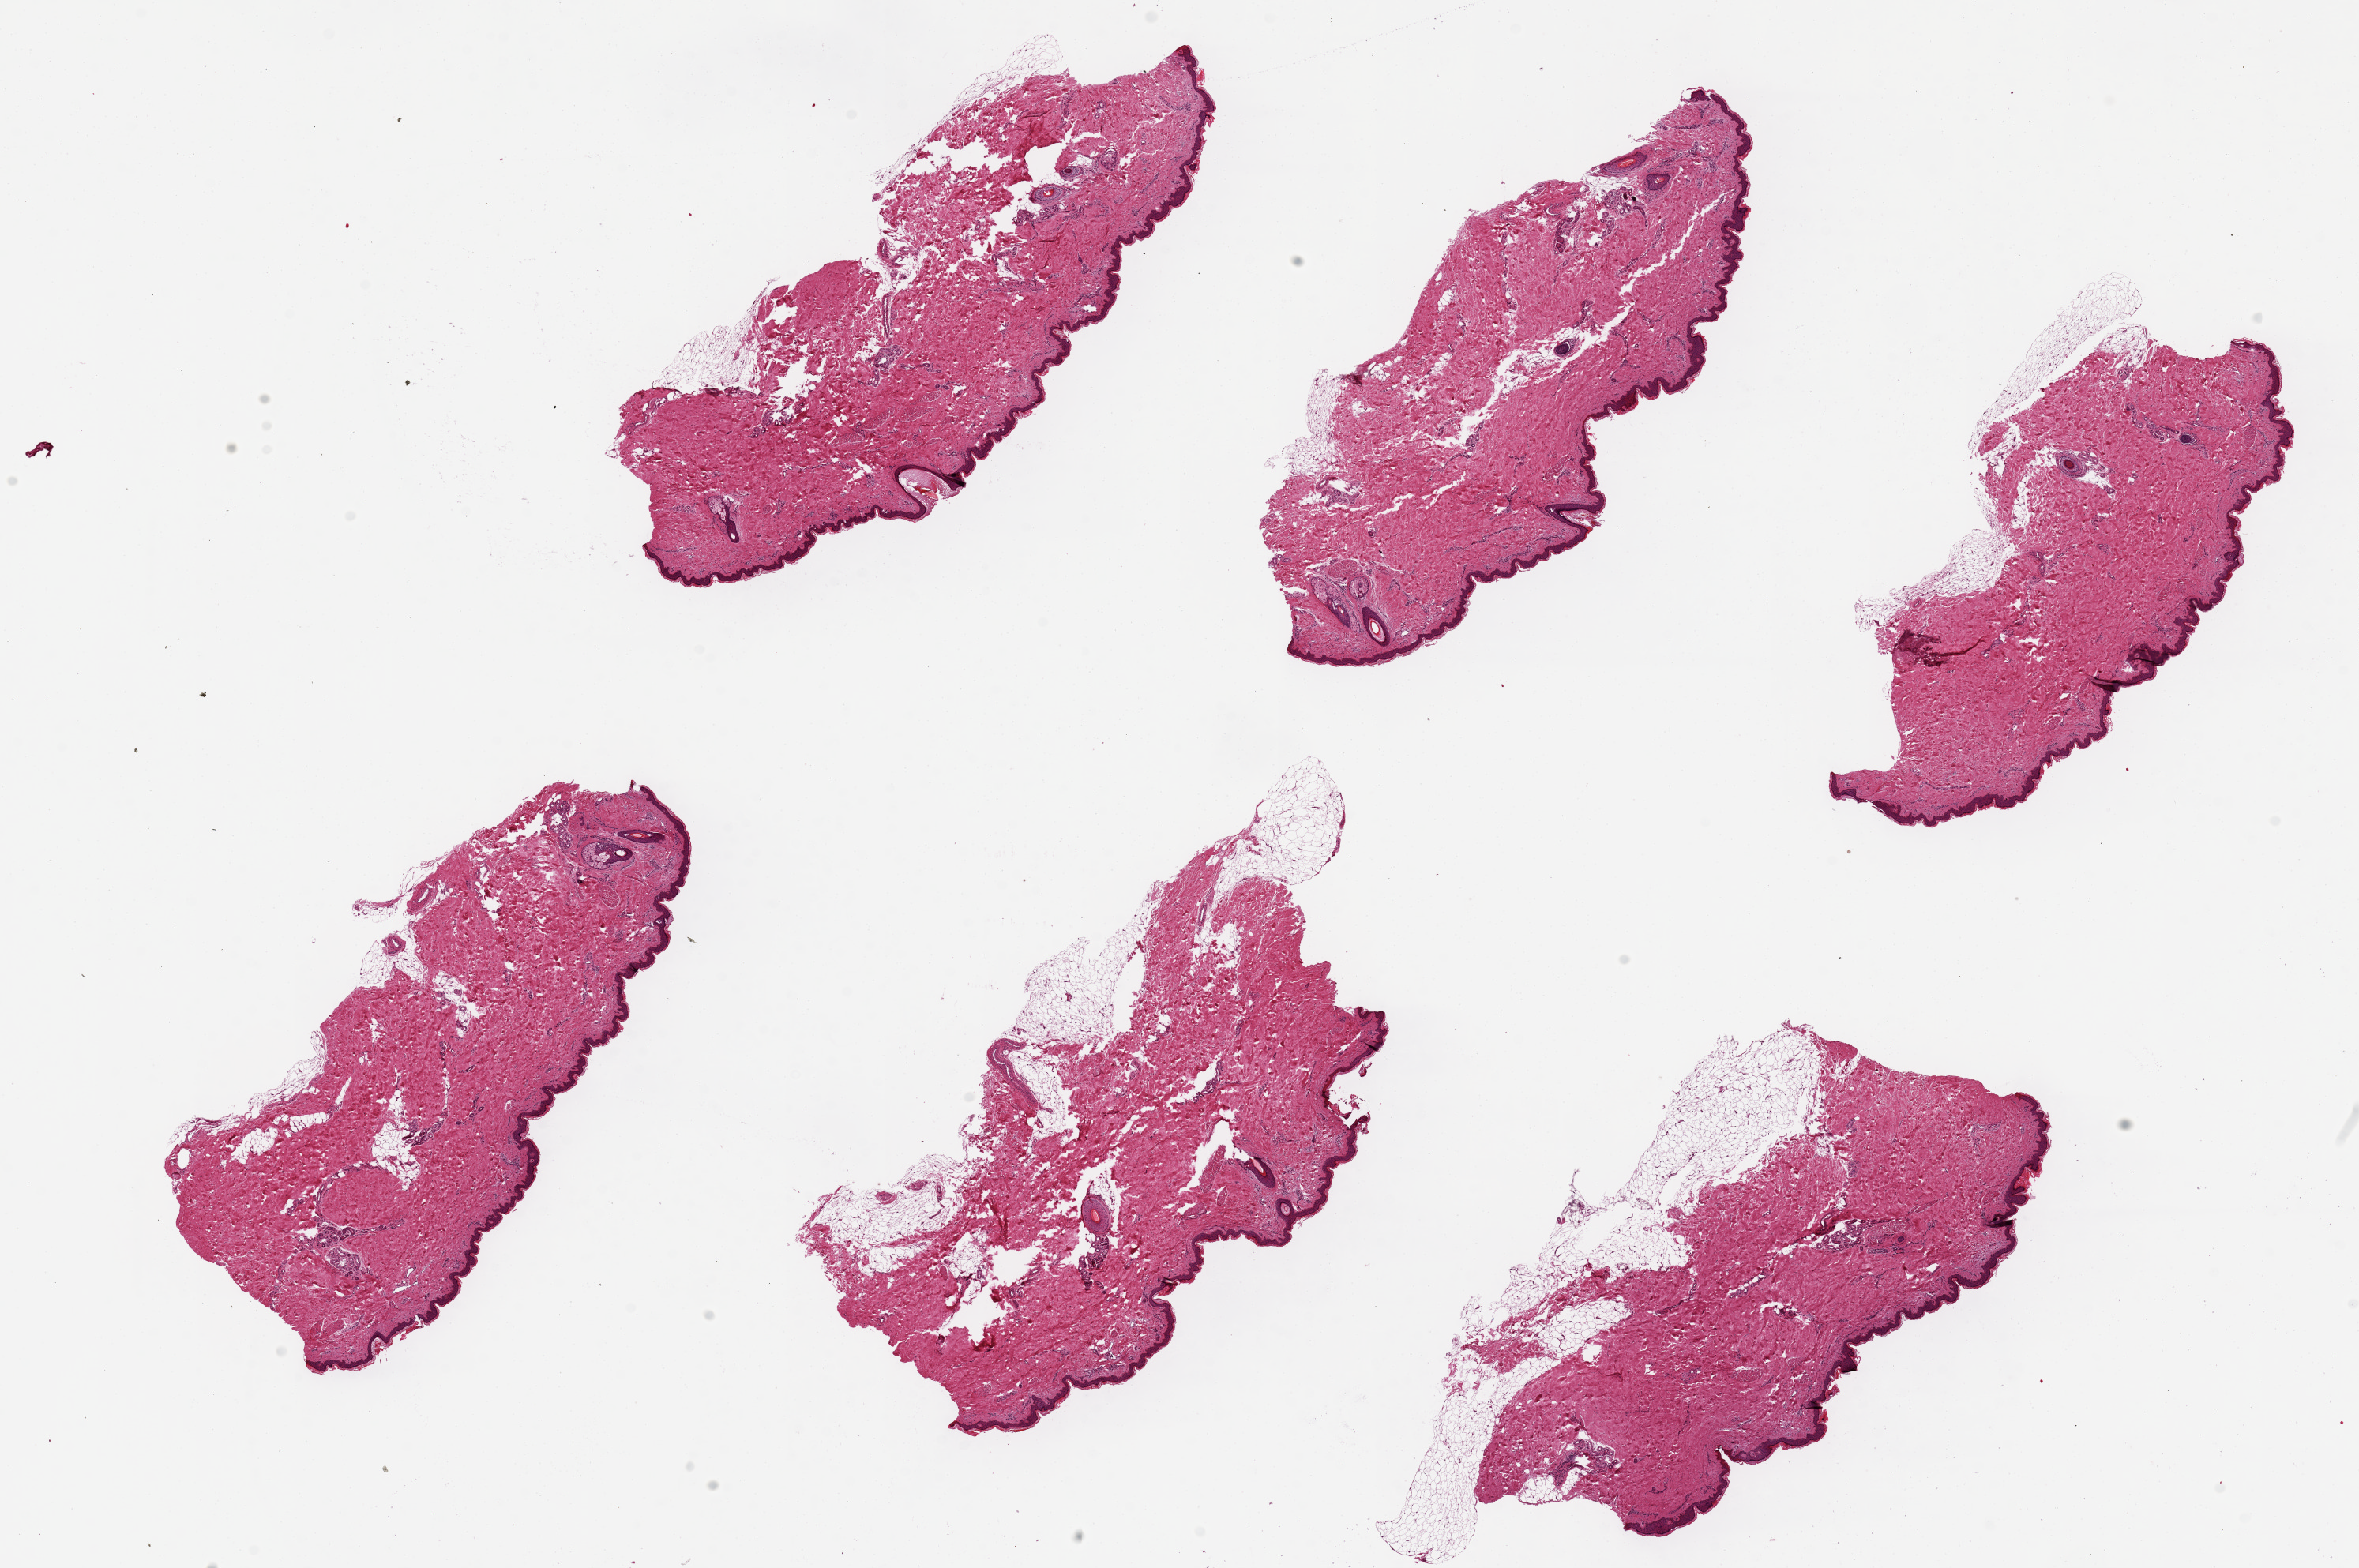
Digitized H&E-stained section, brightfield — whole scanned area (about 23.6 x 15.7 mm, slide scanned at 20x) shown as a low-resolution overview, PAXgene-fixed paraffin-embedded (PFPE) section, section of skin of lower leg (target tissue), tissue donor sample. Male donor.
Reviewer comment on this tissue sample: 6 pieces up to 7x3.5 mm.